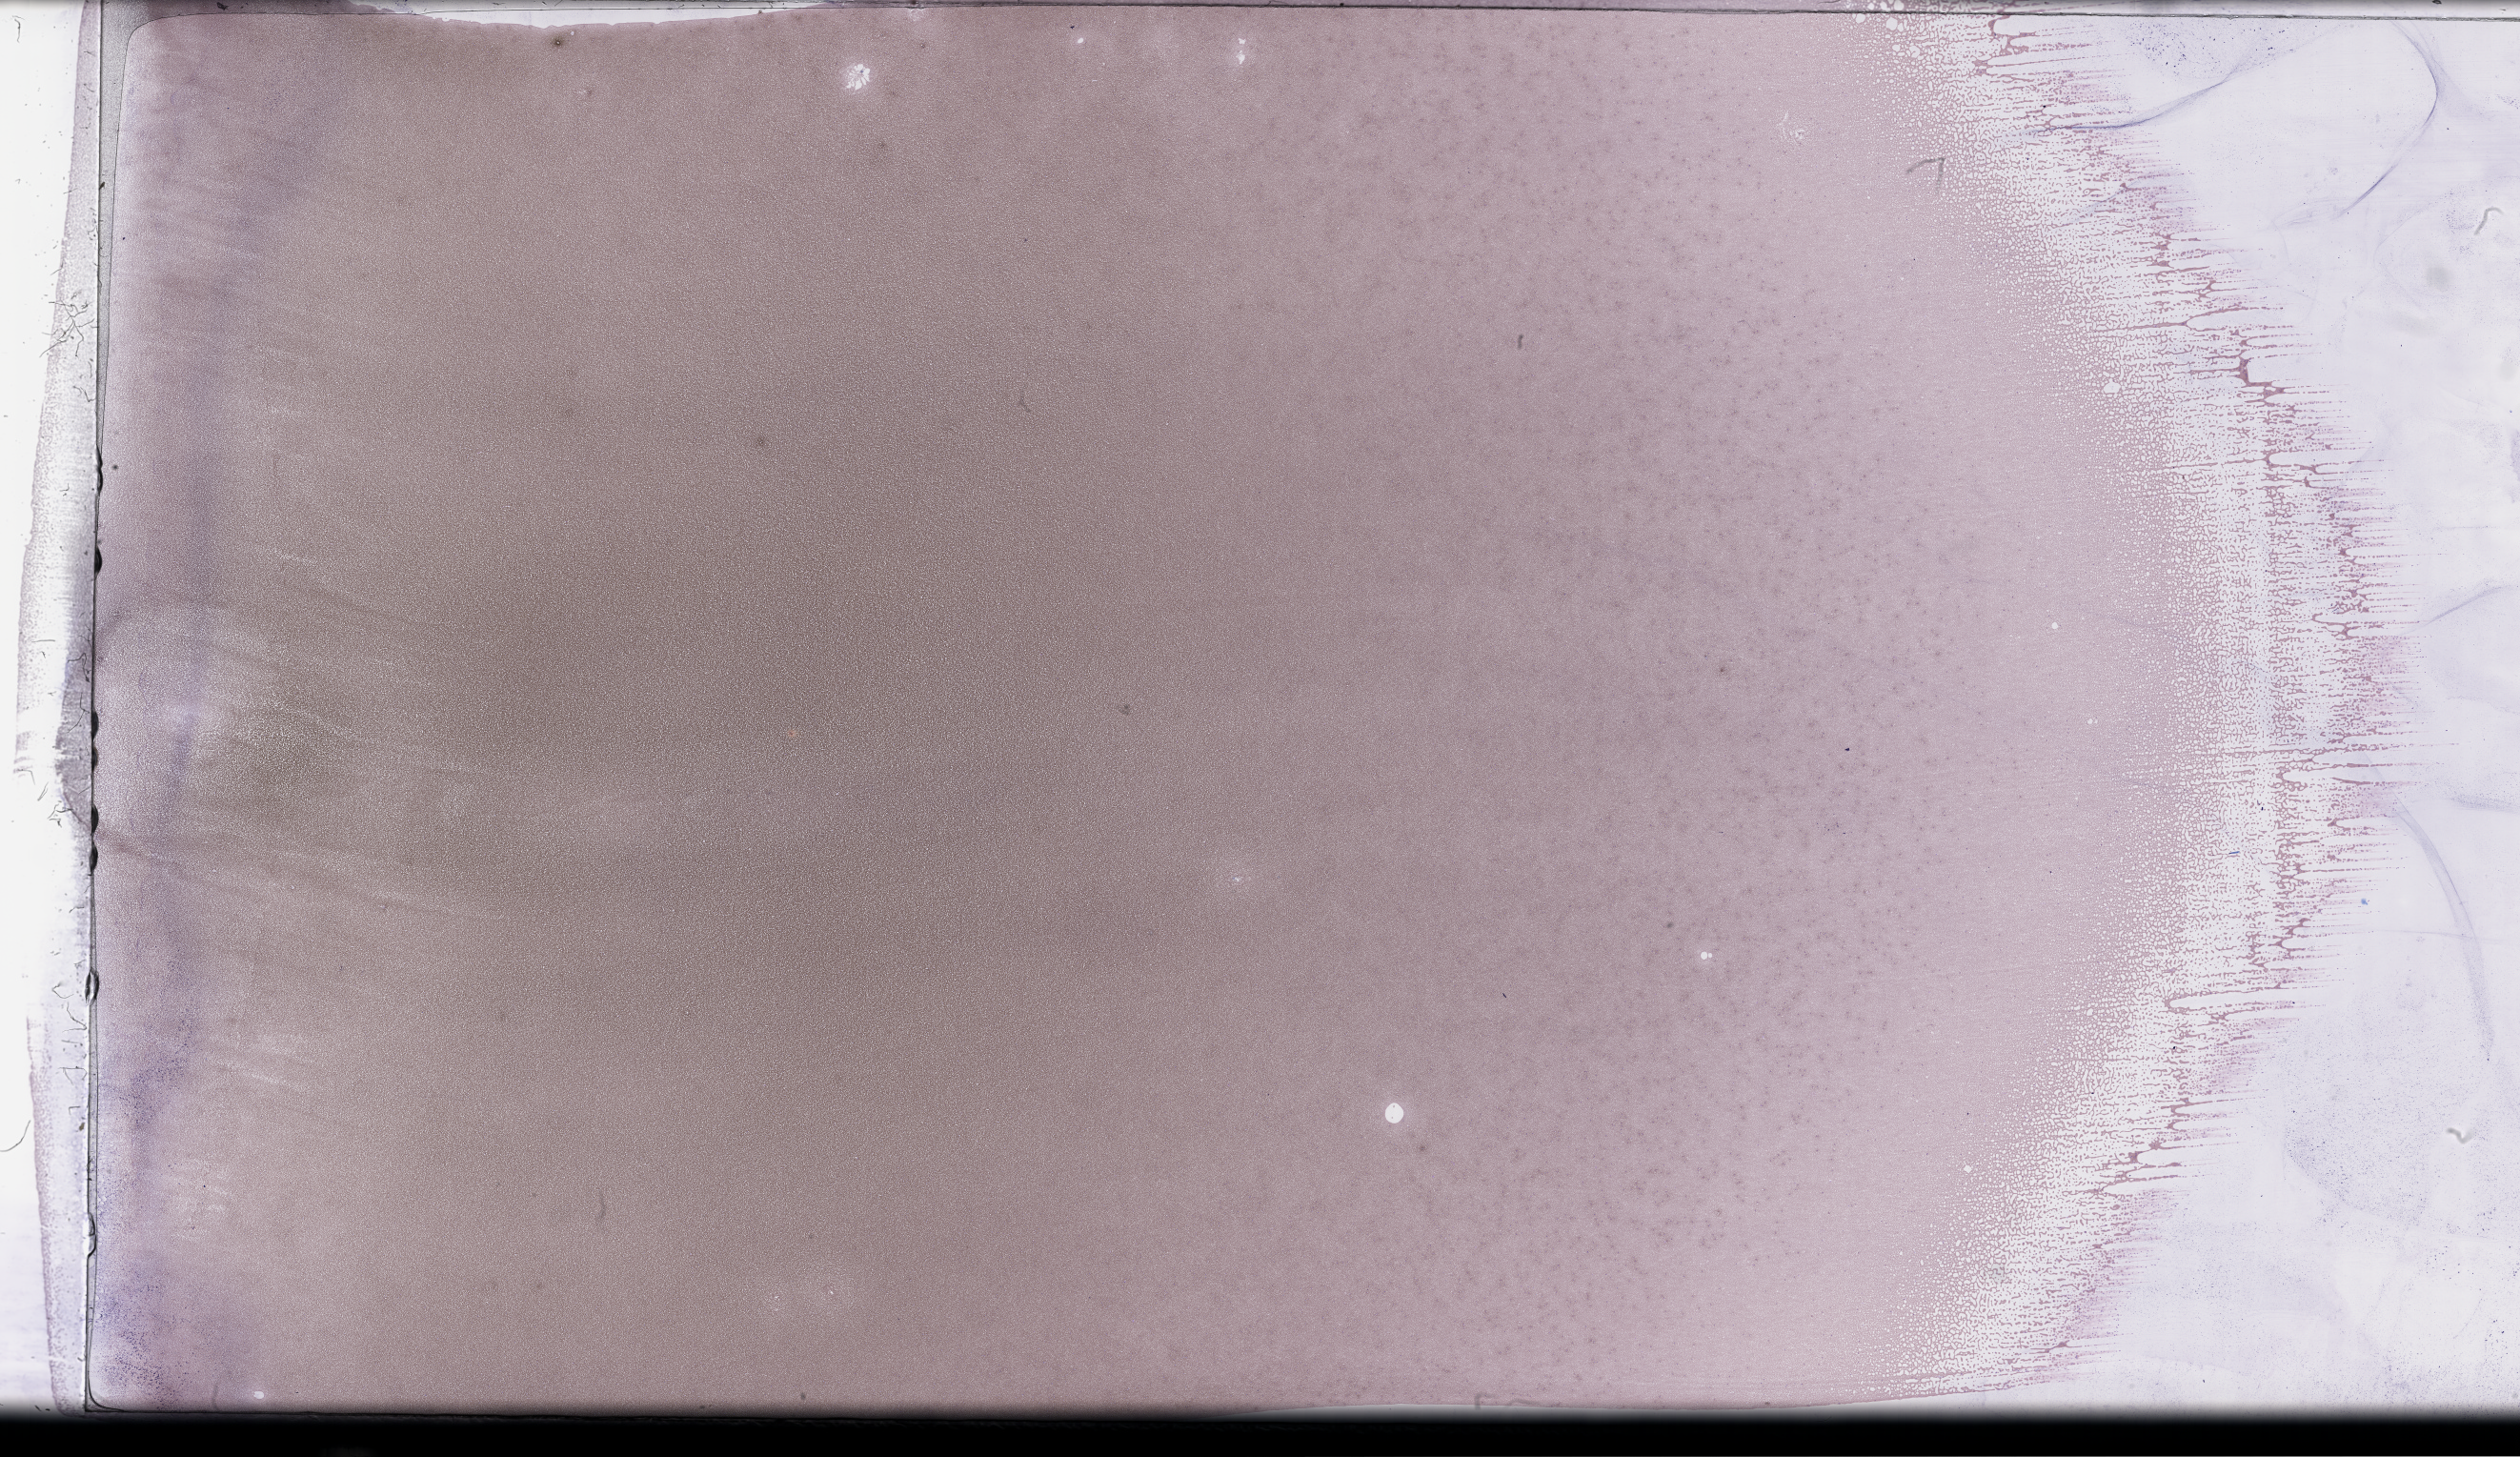
Whole-slide image of a whole blood smear, Wright-Giemsa stain — low-resolution overview of the scanned area, about 42.7 x 24.7 mm, EDTA-anticoagulated smear, collected on treatment. Patient: male.
From a patient with: Plasma Cell Myeloma.